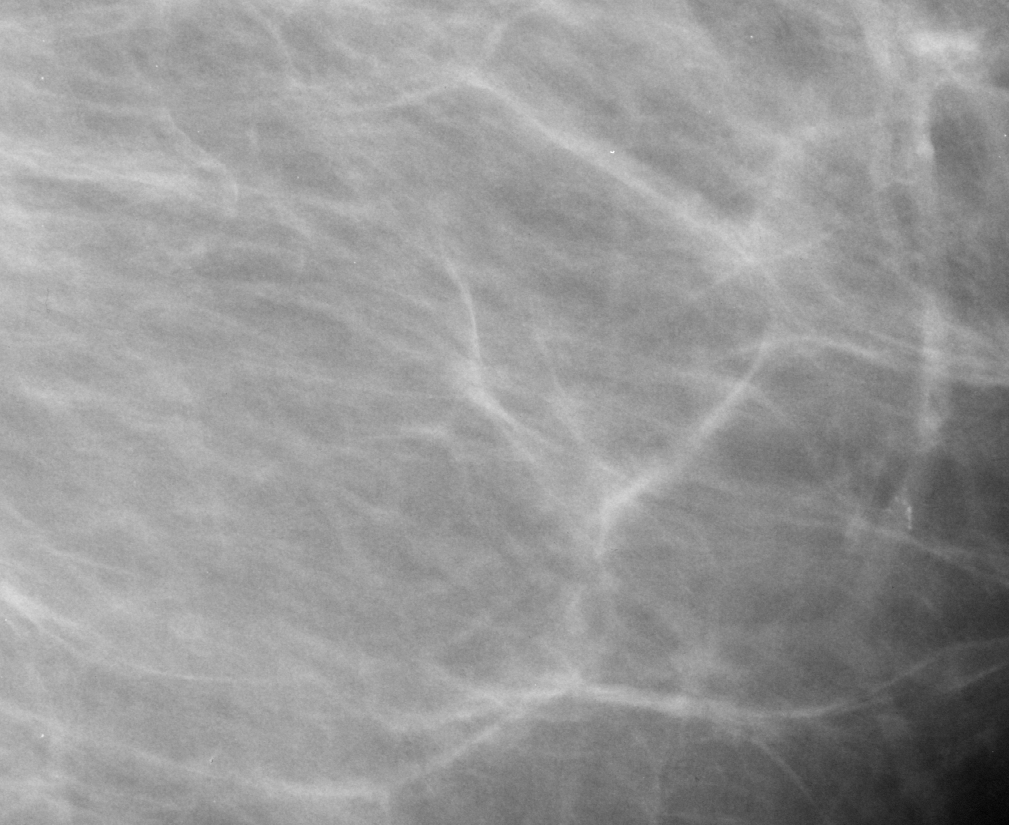
Crop from a digitized film mammogram around one marked abnormality; left breast; MLO view; BI-RADS breast density category 2 (scale 1–4).
- Finding: calcifications, morphology vascular; BI-RADS assessment category 2; subtlety rating 3 on a 1 (subtle) to 5 (obvious) scale; benign; no additional work-up was recommended (benign without callback).